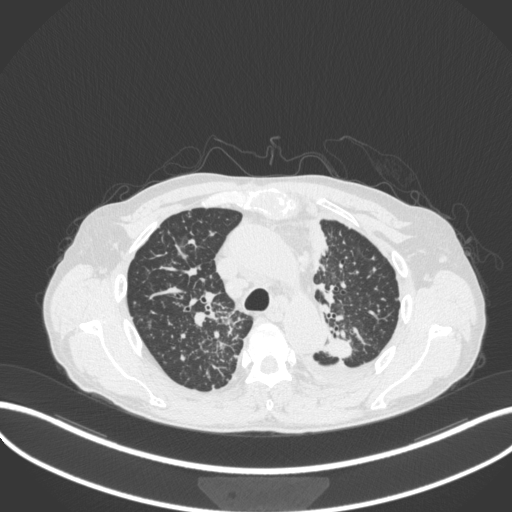
Chest CT, one axial slice; slice 256 of 319 in the series (ordered by position); 120 kVp; lung window (W 1500 / L -600 HU); 1 mm slice thickness; 512 × 512 image matrix. Patient: male, 58 years. Case-level facts recorded for this patient, not image findings: clinical TNM (as recorded): T1c N3 M1.
Annotated regions visible in this slice (rectangle marked by the reading radiologist):
- lung tumour (recorded histology: adenocarcinoma): bounding box [x1, y1, x2, y2] px = [317, 337, 359, 362]